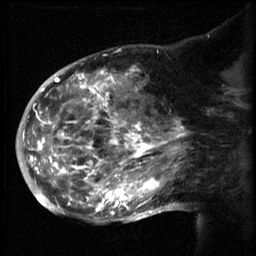
Breast MRI (dynamic contrast-enhanced), one sagittal slice. Slice 36 of 60 in the series (ordered by position). 3 images stored at this slice position (order not interpretable as contrast timing). 1.5 T. TE 4.2 ms, TR 8.2 ms. 256 × 256 image matrix. Patient: female, 50 years.
Outlined on this slice (semi-automatically segmented with operator editing):
- analysis volume of interest (the breast-tissue region the enhancement analysis was run in; not a lesion): bounding box <50,64,169,217> (left, top, right, bottom; pixels)
- tumour enhancement mask (voxels above the 70 % enhancement threshold inside the analysis volume of interest): <50,68,169,215>